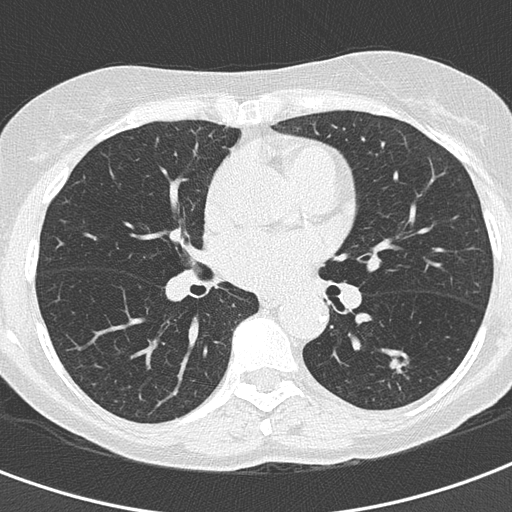
Low-dose screening chest CT, axial slice. Second annual screen. Lung window (W 1500 / L -600 HU). Slice 76 of 155 in the series. 512 × 512 image matrix. Female, age 60 years at enrolment. Current smoker at enrolment.
Expert reader's lesion annotation, box from (x=378, y=346) to (x=413, y=377) px. Screening reader's record for this exam (one nodule recorded; not confirmed to be the boxed lesion): non-calcified nodule or mass ≥4 mm, left lower lobe, 10 × 9 mm, soft tissue attenuation. Participant outcome: lung cancer diagnosed 64 days after this screen — adenocarcinoma, NOS, left lower lobe, well differentiated (G1), stage IA (AJCC 6th edition), 15 mm at pathology.